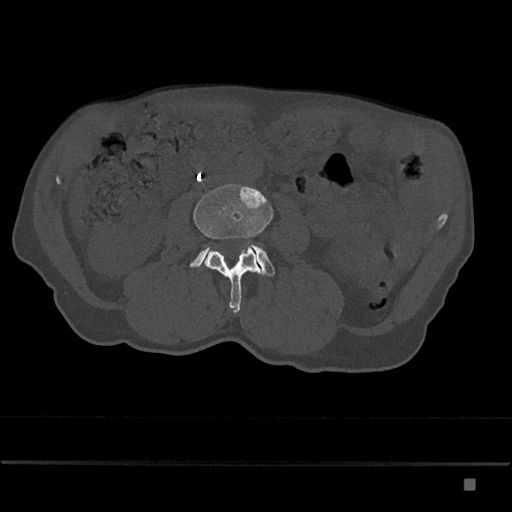
CT including the spine, one axial slice; position 385 of 797 along the scan axis; 120 kVp; bone window (W 1800 / L 400 HU); 0.5 mm slice thickness; 512 × 512 image matrix, field of view 390 × 390 mm. Patient: male, 72 years. From the clinical record (not read from this slice): primary cancer: prostate.
Outlined on this slice (semi-automatic segmentation, software-assisted and operator-edited):
- L3 vertebra: bounding box [x1, y1, x2, y2] px = [193, 184, 273, 313]
- L4 vertebra: [190, 244, 275, 276]